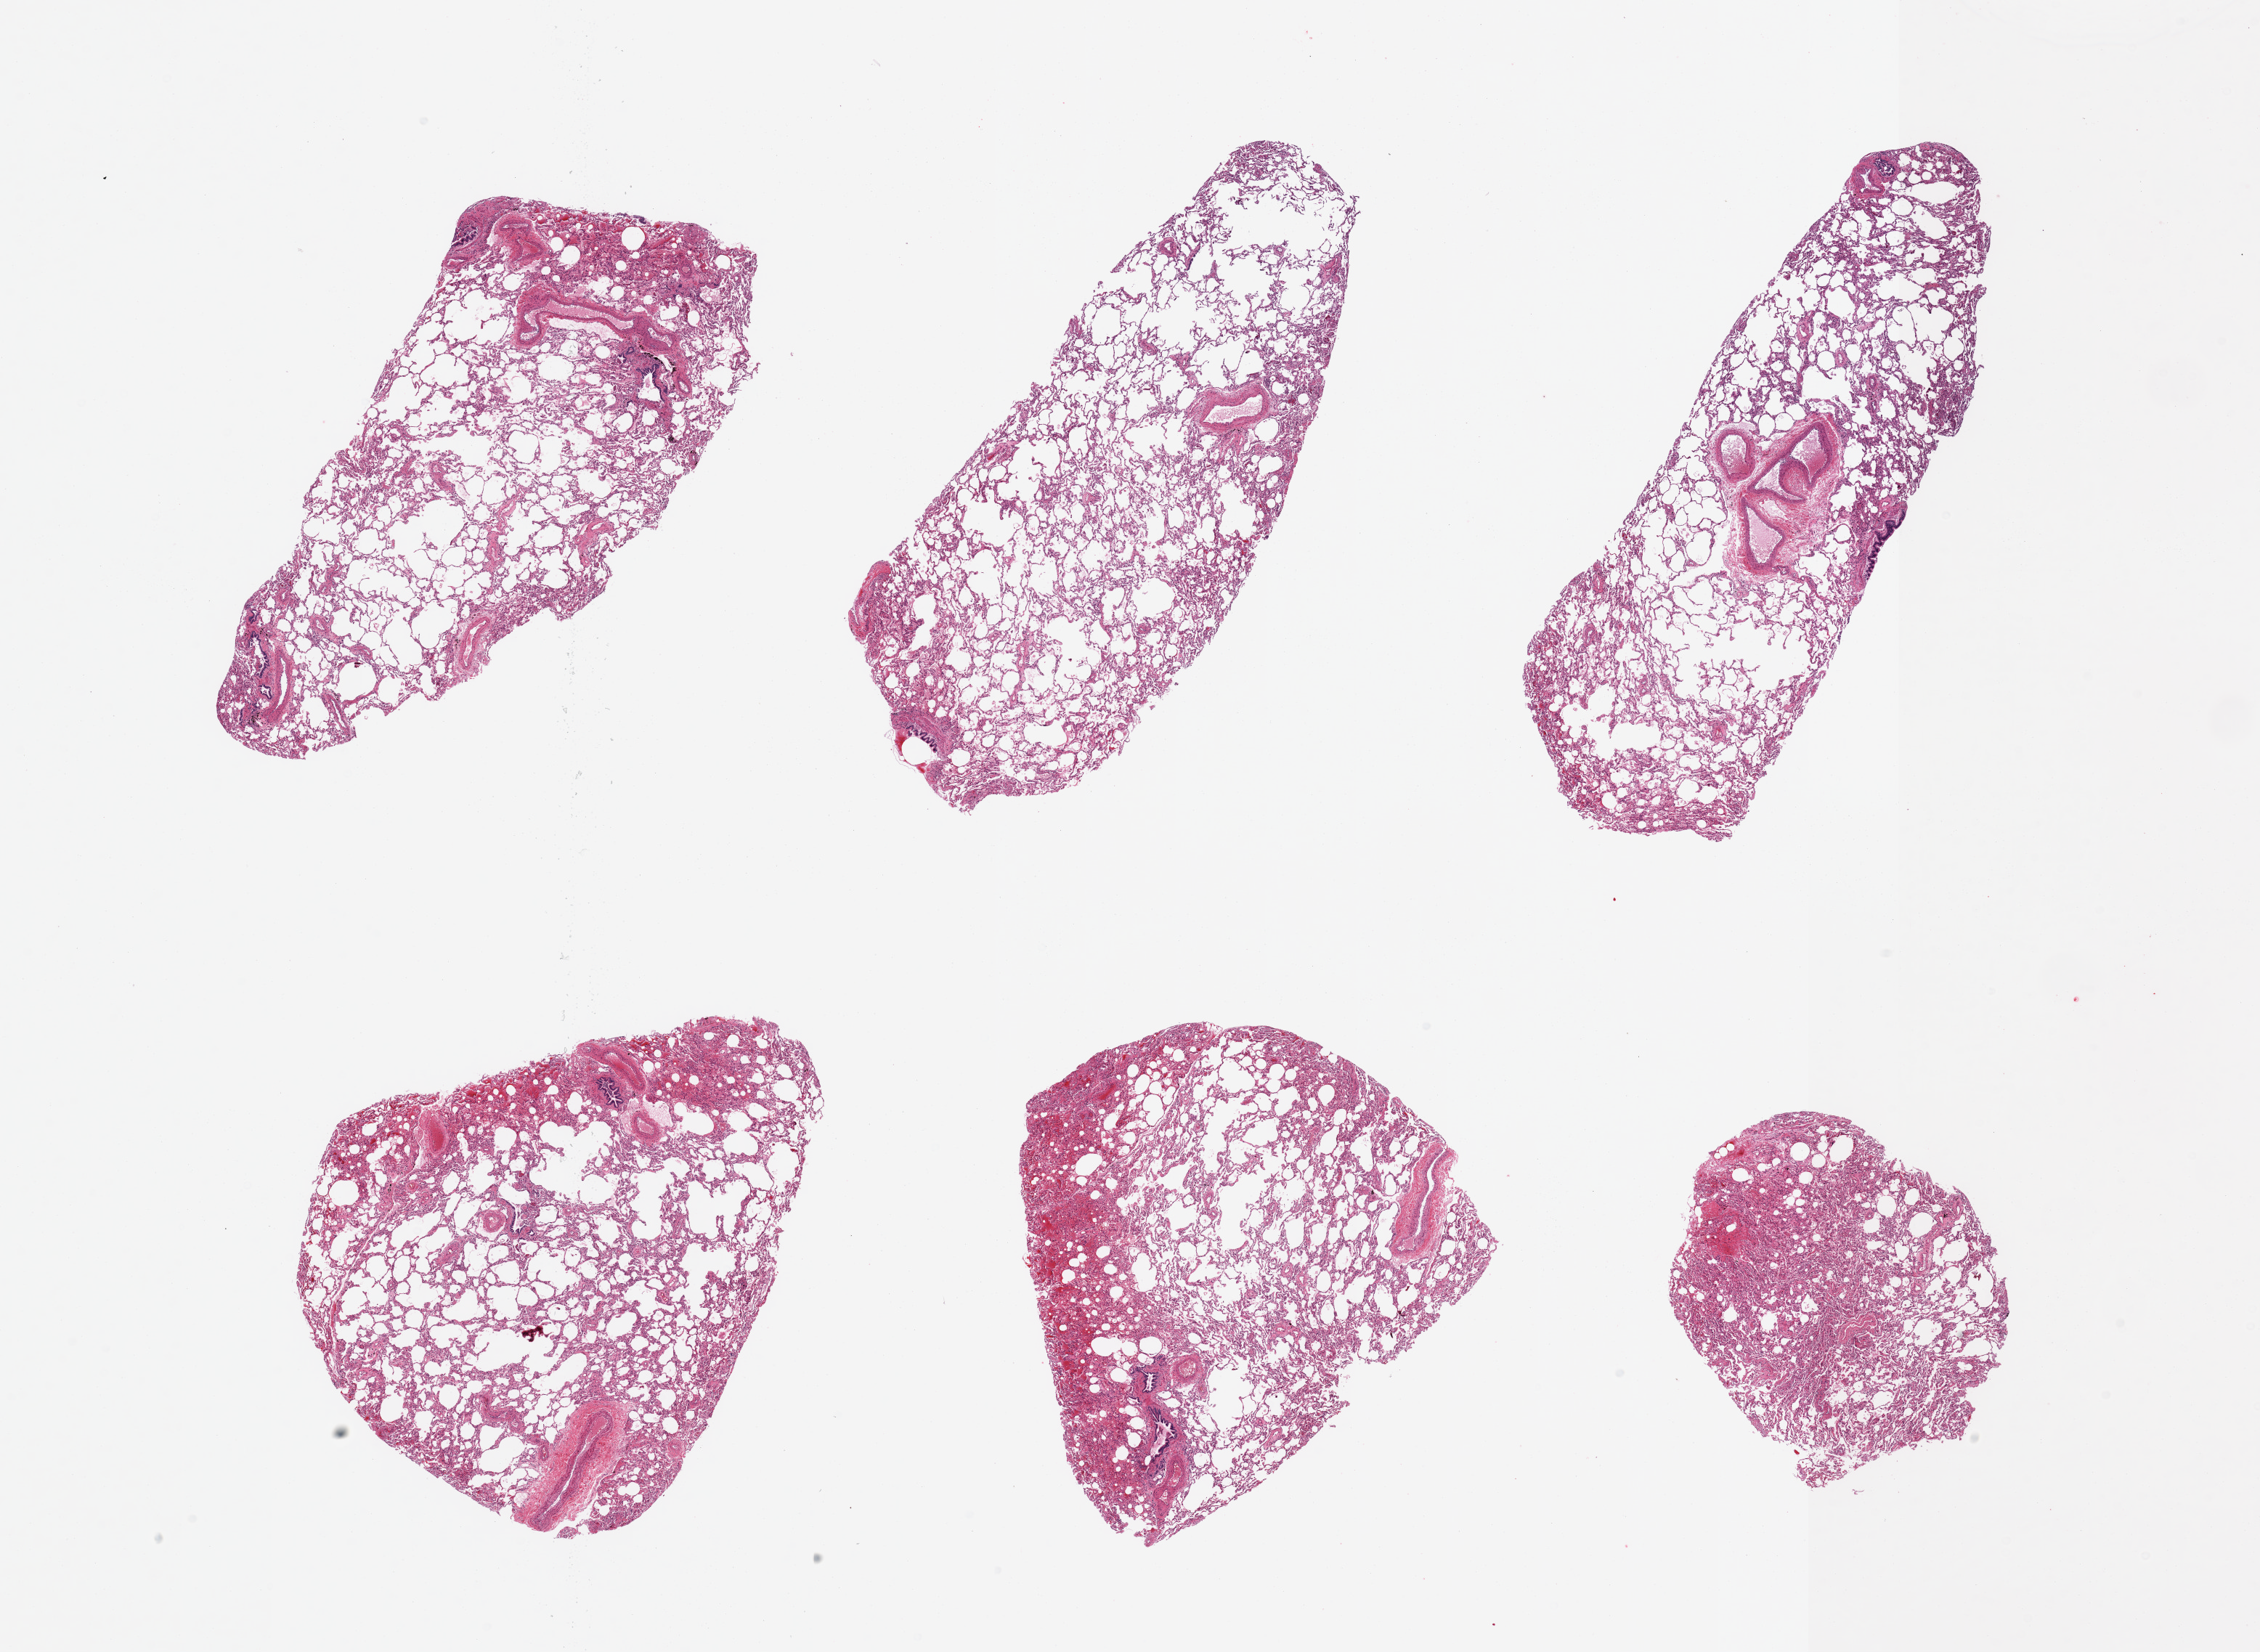
Digitized H&E-stained section, brightfield, low-resolution overview of the scanned area, about 24.6 x 18.0 mm (acquisition: 20x scan); PAXgene-fixed, paraffin-embedded tissue; section of lung (target tissue); tissue donor sample. Male donor.
Reviewer comment on this tissue sample: 6 pieces; patchy intra-alveolar red blood cell extravasation and fresh hemorrhage; patchy neutrophilic infiltration of alveolar septa and intra-alveolar aggregates of neutrophils.